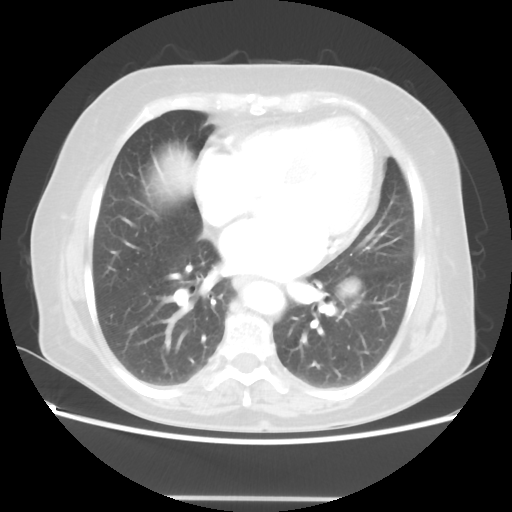
Chest CT, one axial slice; slice 24 of 56 in the series (ordered by position); 100 kVp; lung window (W 1500 / L -600 HU); 5 mm slice thickness; 512 × 512 image matrix, field of view 360 × 360 mm. Patient: female, 73 years. Case-level facts recorded for this patient, not image findings: clinical TNM (as recorded): T1c N0 M0.
Annotated regions visible in this slice (bounding box drawn by a radiologist):
- lung tumour (recorded histology: adenocarcinoma): bounding box (x1, y1, x2, y2) in pixels: (343, 281, 354, 298)